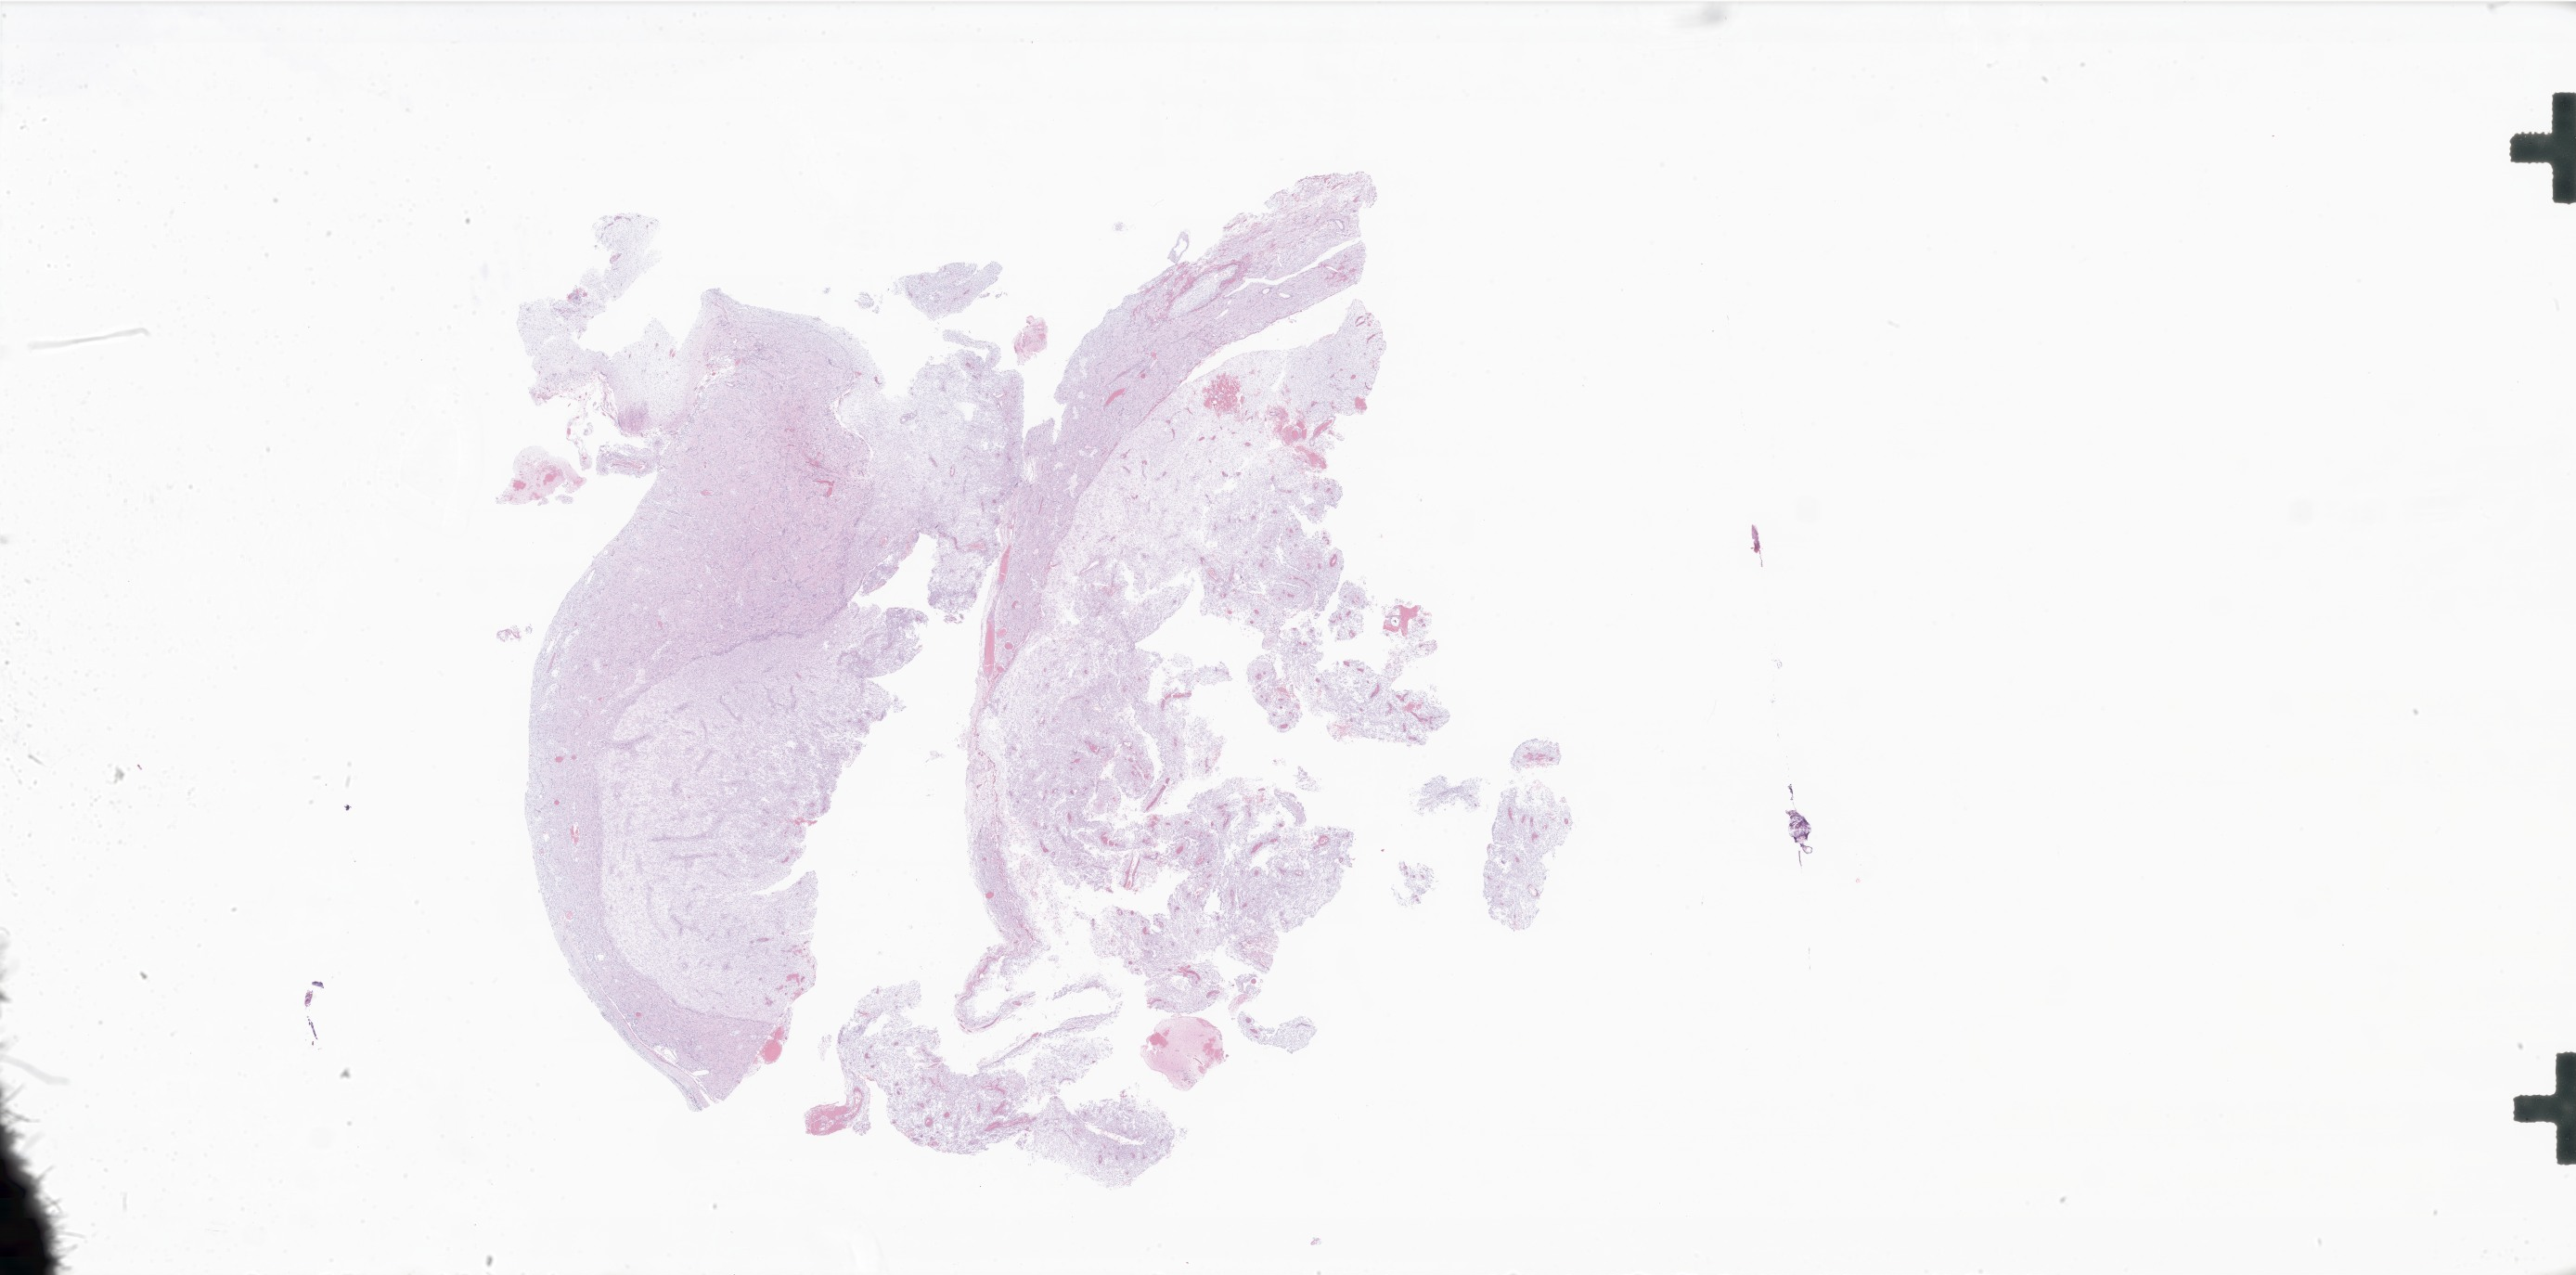
Hematoxylin and eosin (H&E) whole-slide image of tumor tissue from the brain, a low-resolution overview of the entire scanned area, about 46.8 x 23.2 mm; formalin-fixed paraffin-embedded section. Patient female; age 594 days (about 1.6 years).
• diagnosis: Pilocytic astrocytoma